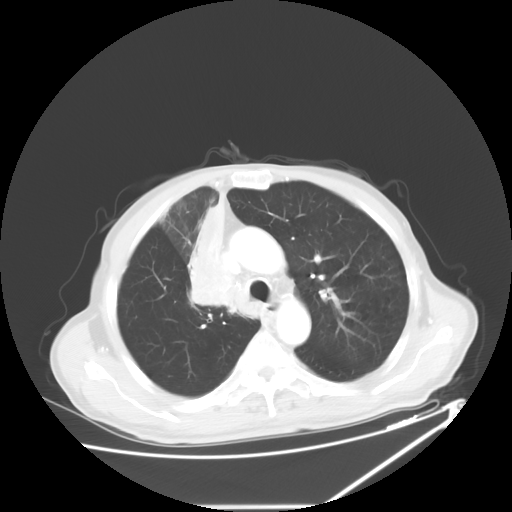
Chest CT, one axial slice; position 43 of 60 along the scan axis; reconstruction kernel STANDARD; 120 kVp; lung window (W 1500 / L -600 HU); 512 × 512 image matrix. Patient: male, 73 years. From the clinical record (not read from this slice): clinical TNM (as recorded): T2a N1 M0.
Structures marked on this image (rectangle marked by the reading radiologist):
- lung tumour (recorded histology: squamous cell carcinoma): bounding box [x1, y1, x2, y2] px = [189, 182, 237, 309]